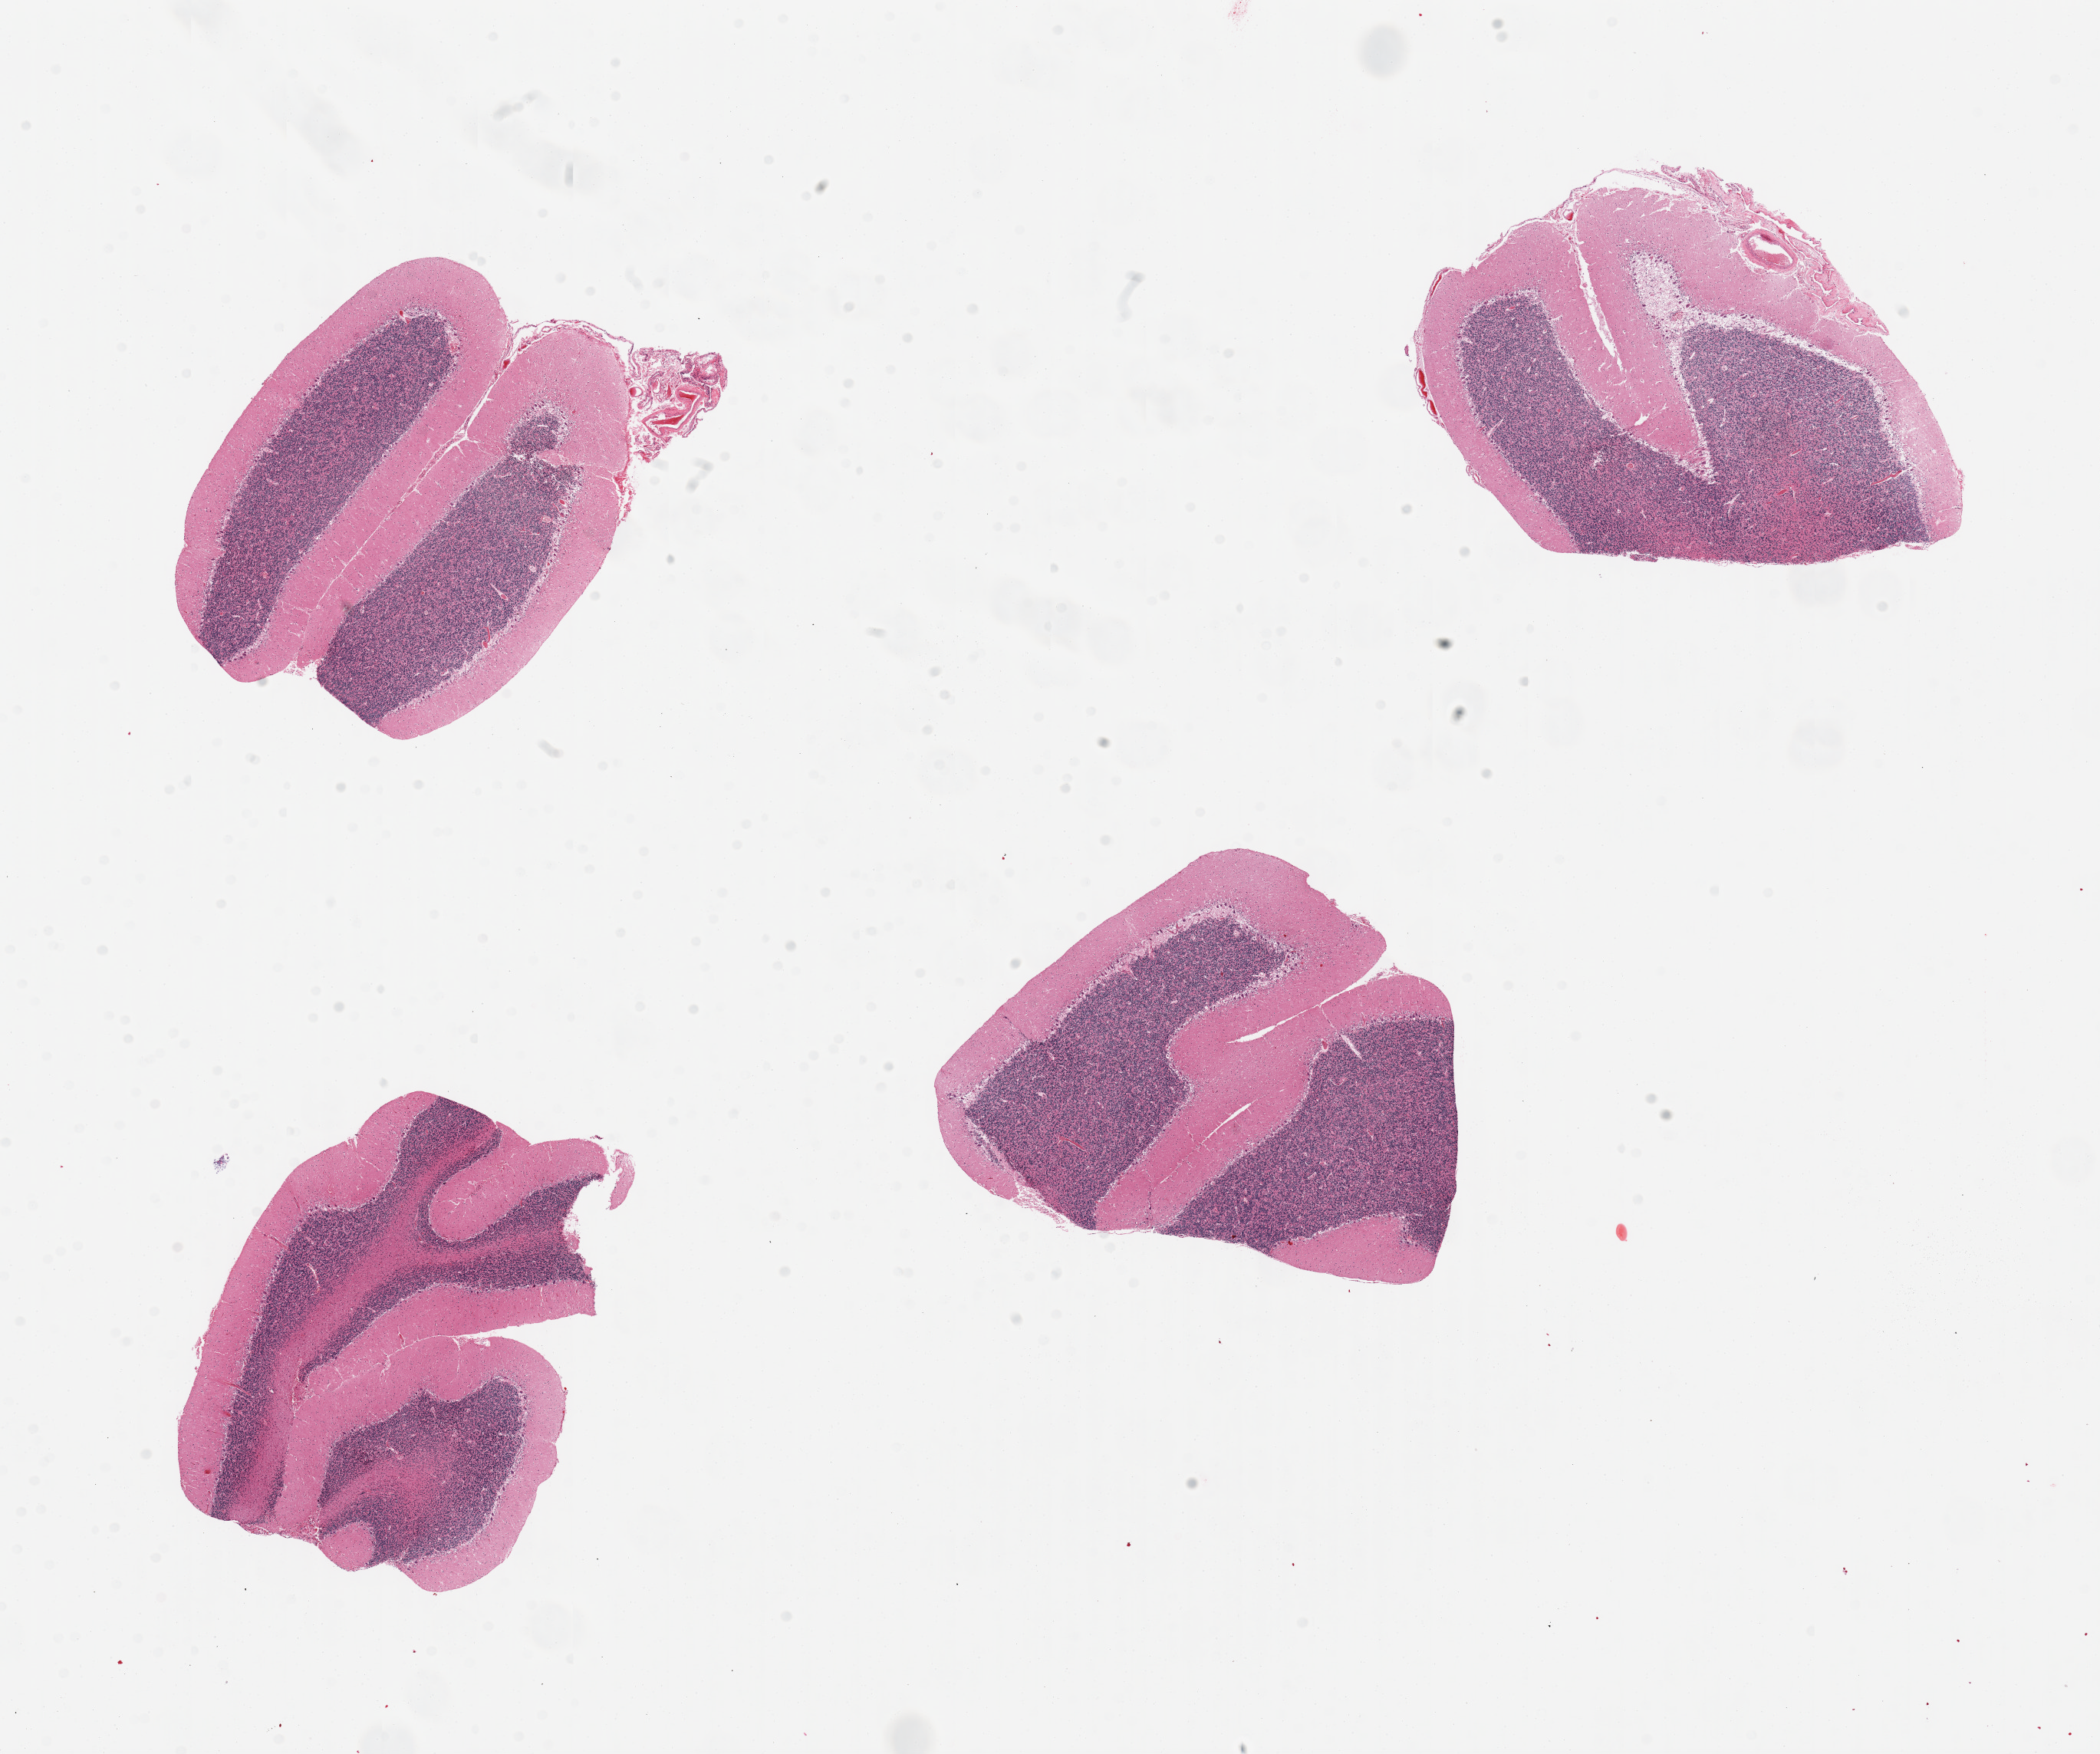
H&E whole-slide image — a low-resolution overview of the entire scanned area, about 21.7 x 18.1 mm (acquisition: 20x scan), PAXgene-fixed, paraffin-embedded tissue, section of cerebellum (target tissue), donor tissue sample. Donor: male.
* reviewer comment on this tissue sample: 4 pieces, no abnormalities noted